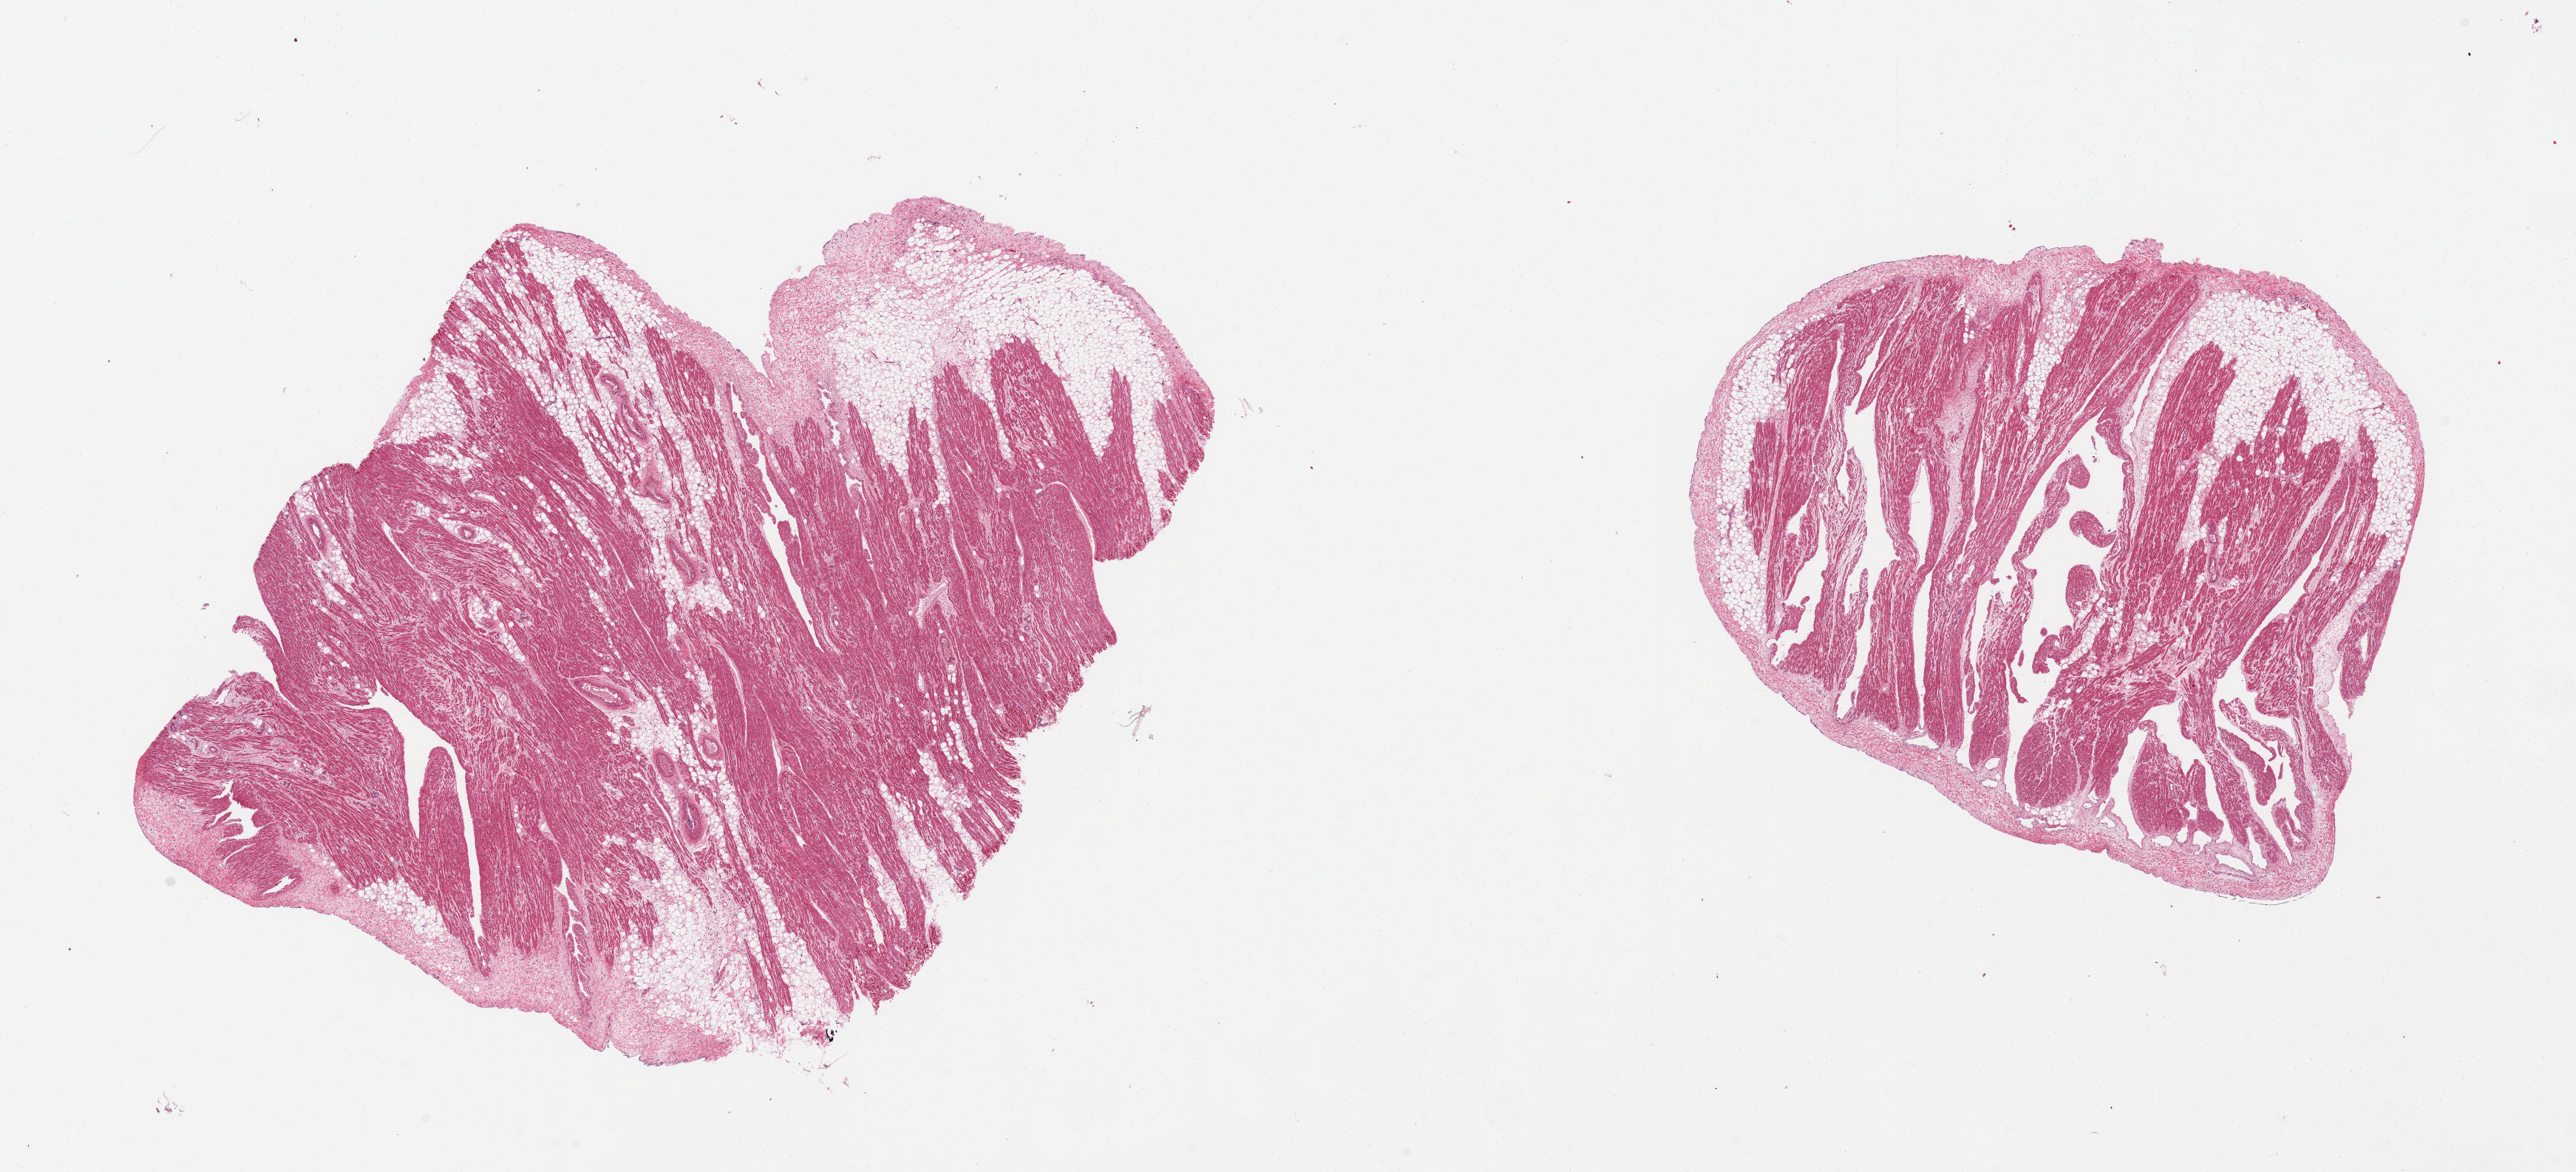
Whole-slide image, haematoxylin and eosin stain, low-resolution overview of the scanned area, about 27.6 x 12.5 mm, PAXgene-fixed, paraffin-embedded tissue, section of auricular appendage (target tissue), tissue donor sample. Donor sex: female.
Reviewer comment on this tissue sample: 2 pieces, 10-20% fat.